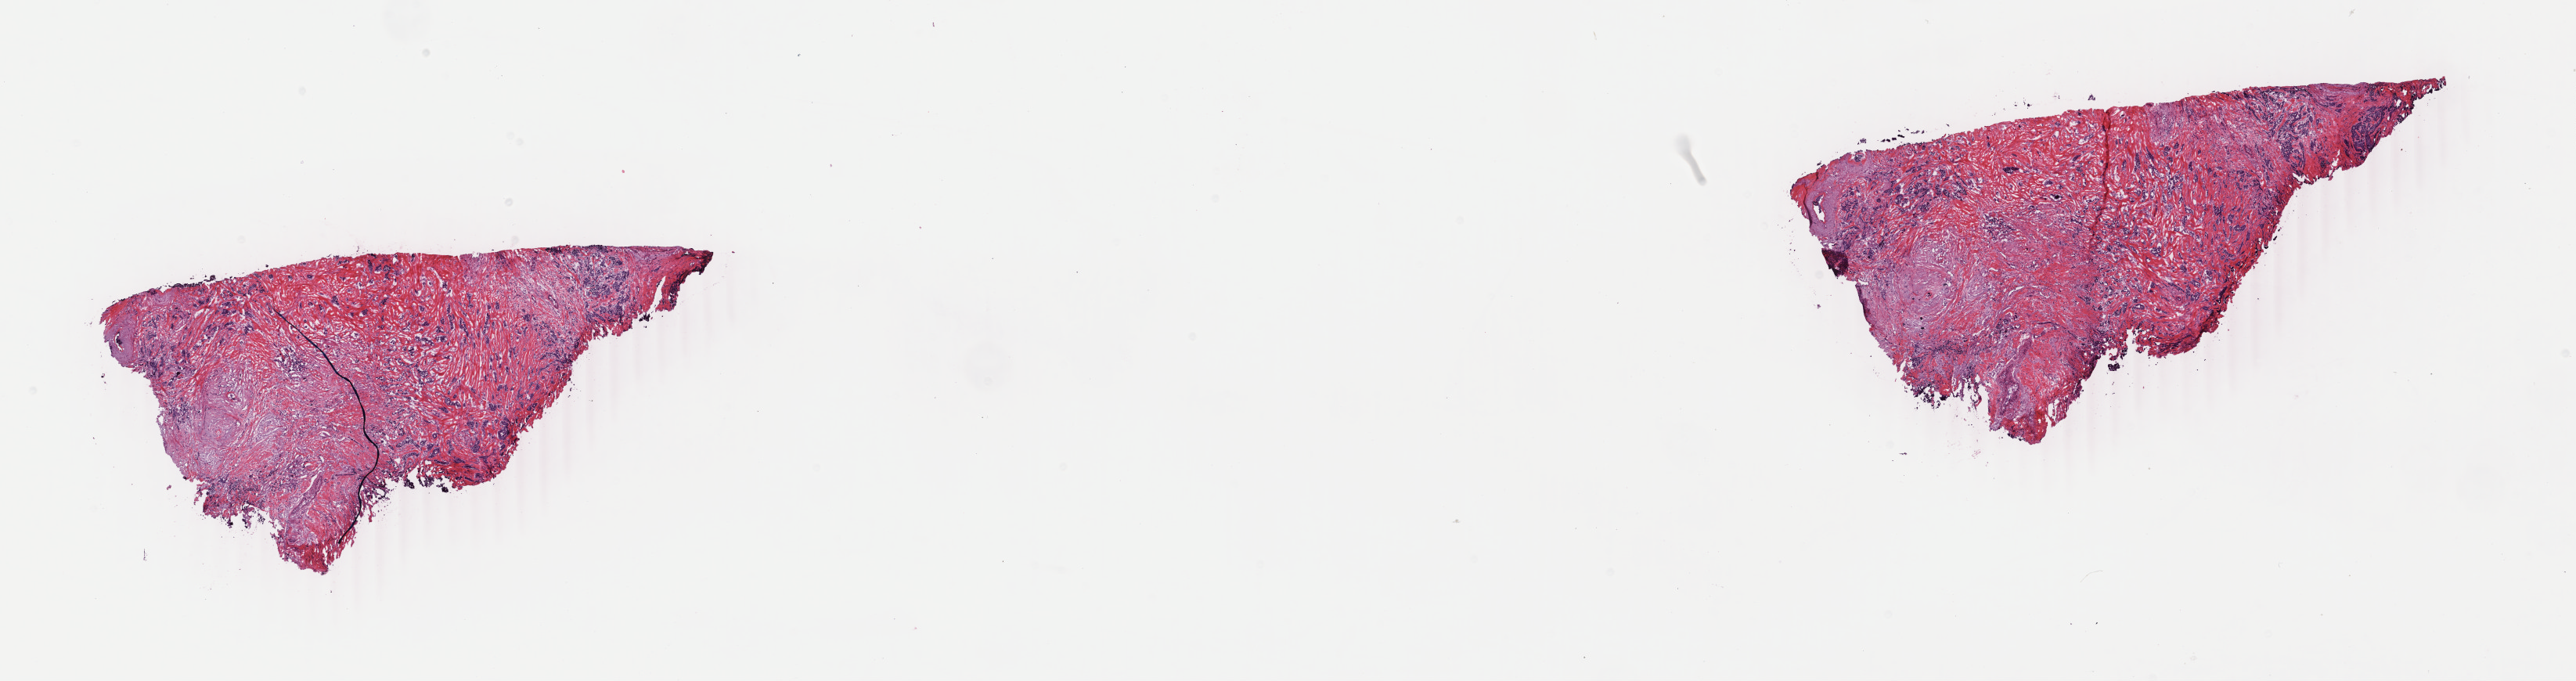
Whole-slide histology image, H&E-stained — whole scanned area (about 26.2 x 6.9 mm) shown as a low-resolution overview; frozen section from the top of the tissue portion; primary tumour sample from the breast. Patient: female, age at initial diagnosis 73 years. Slide review estimates, as recorded: tumour cells 62%, tumour nuclei 80%, normal cells 0%, stromal cells 37%, necrosis 1%. Inflammatory infiltration, as recorded: lymphocyte infiltration 1%, monocyte infiltration 0%, neutrophil infiltration 0%.
• laterality: left
• lymph nodes positive (case pathology): 2 of 15 examined
• histologic diagnosis: Infiltrating duct and lobular carcinoma